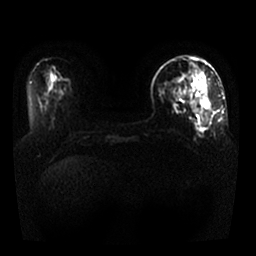
Breast MRI, one axial slice; slice 11 of 25 in the series (ordered by position); diffusion-weighted series; image 2 of 4 stored at this slice position (different b-values; order by instance number); 1.5 T; 4 mm slice thickness; 256 × 256 image matrix, field of view 330 × 330 mm. Female patient.
Outlined on this slice (expert manual segmentation):
- tumour on diffusion-weighted imaging: bounding box (x1, y1, x2, y2) in pixels: (205, 101, 209, 109)